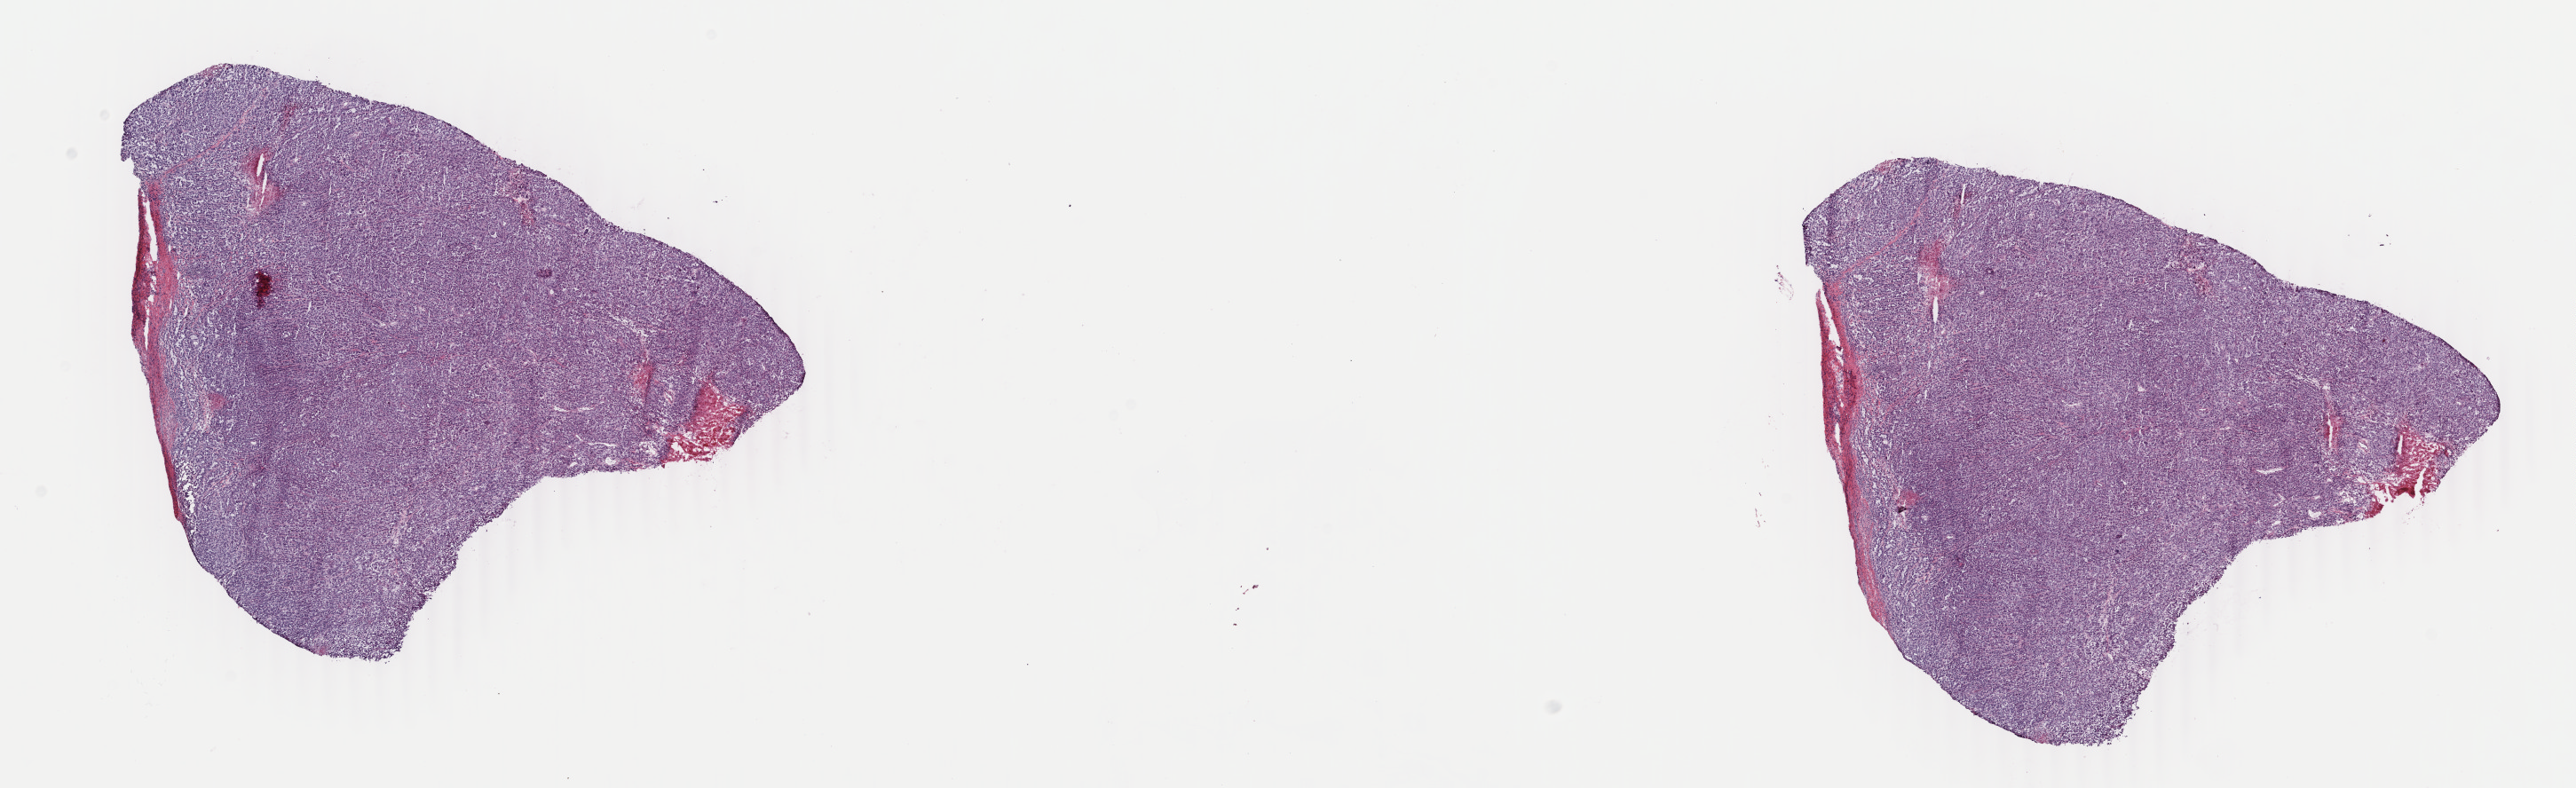
Digitized H&E-stained tissue section (whole slide) — a low-resolution overview of the entire scanned area, about 23.1 x 7.1 mm; frozen section; metastatic tumour sample, sampled site: lymph nodes of axilla or arm. Patient: male, age at initial diagnosis 56 years.
This section: metastatic tumour tissue. Patient diagnosis: Malignant melanoma, NOS.